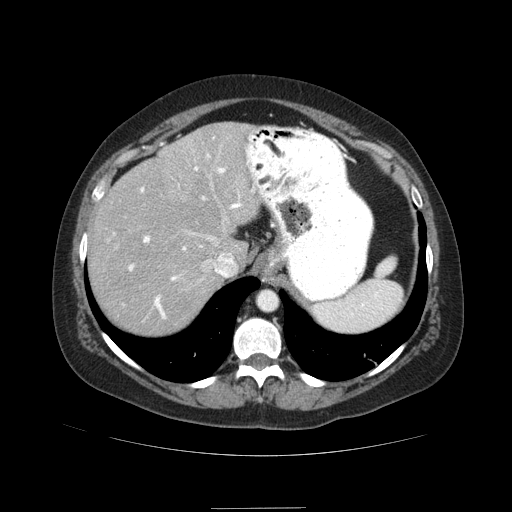
Contrast-enhanced abdominal CT (liver protocol), one axial slice. Slice 67 of 89 in the series (ordered by position). Soft-tissue window (W 400 / L 40 HU). 2.5 mm slice thickness. 512 × 512 image matrix, field of view 400 × 400 mm. Case-level facts recorded for this patient, not image findings: diagnosis: hepatocellular carcinoma (patient treated with transarterial chemoembolisation; whether this scan precedes or follows treatment is not stated here); TNM stage (as recorded): Stage-IIIB.
Annotated regions visible in this slice (semi-automatic segmentation, software-assisted and operator-edited):
- abdominal aorta: bounding box [x1, y1, x2, y2] px = [258, 291, 277, 310]
- liver parenchyma outside the tumour (the mass and vessels are separate outlines, so this box may not span the whole liver): [88, 122, 259, 334]
- liver vessels: [128, 154, 242, 319]